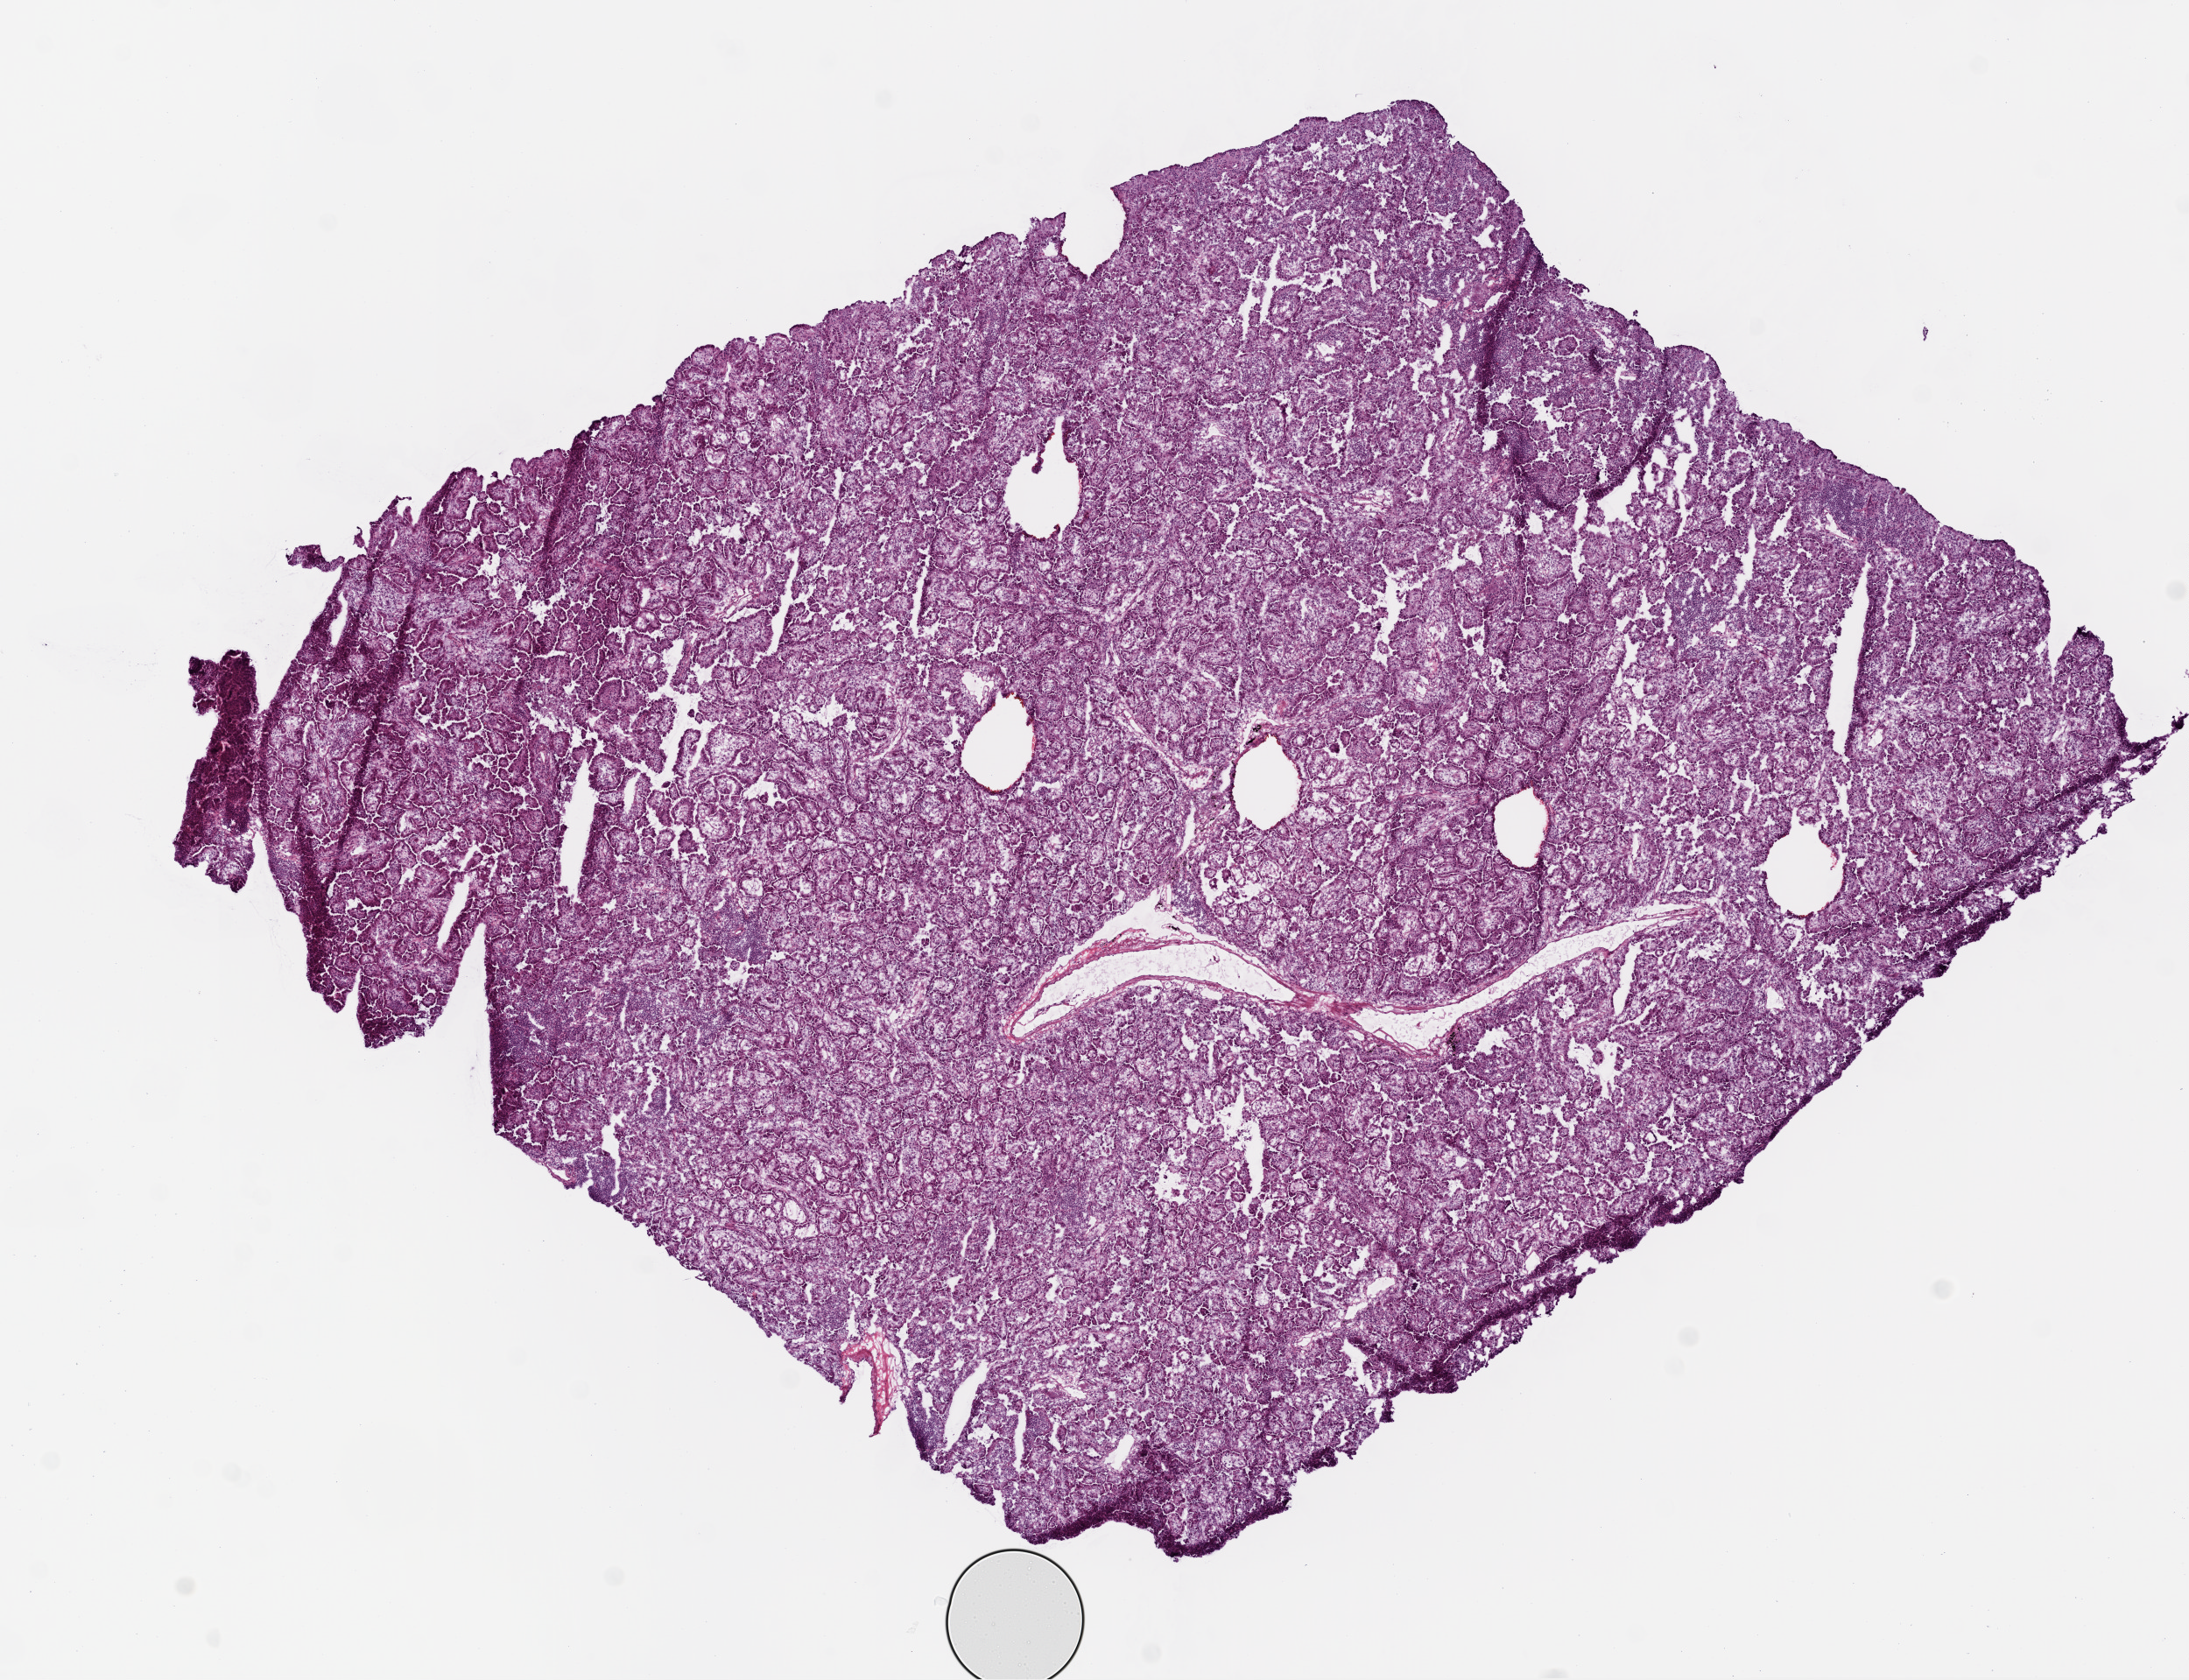
Hematoxylin and eosin (H&E) stained whole-slide image — a low-resolution overview of the entire scanned area, about 10.0 x 7.7 mm (acquisition: 20x scan), frozen section from the top of the tissue portion, lung, primary tumour sample. Male patient; age at initial diagnosis 67 years. Slide review estimates, as recorded: tumour cells 100%, tumour nuclei 85%, normal cells 0%, stromal cells 0%, necrosis 0%. Inflammatory infiltration, as recorded: lymphocyte infiltration 5%, monocyte infiltration 10%, neutrophil infiltration 0%.
TNM: T2b N0 M0. Laterality: right. Pathologic diagnosis: Papillary adenocarcinoma, NOS (upper lobe, lung). AJCC pathologic stage: IIA (7th edition).